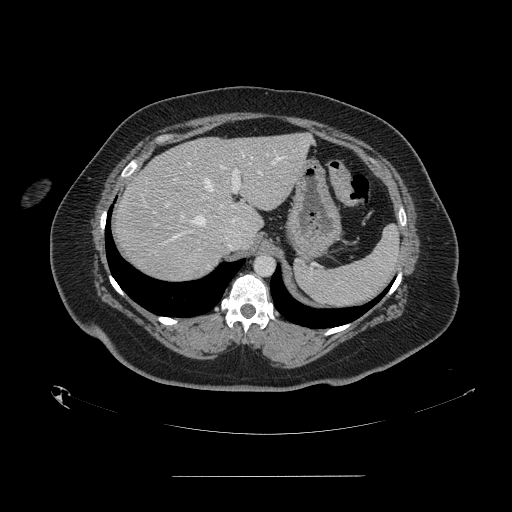
Contrast-enhanced abdominal CT, one axial slice; slice 113 of 164 in the series (ordered by position); 120 kVp; intravenous contrast given; soft-tissue window (W 400 / L 40 HU); 2.5 mm slice thickness; 512 × 512 image matrix. Female patient, age 52 years. Case-level facts recorded for this patient, not image findings: diagnosis: colorectal cancer liver metastases, imaged before liver resection; multiple liver metastases: yes; largest metastasis: 3.5 cm; disease in both lobes: no.
Outlined on this slice (outlined manually by an expert reader):
- hepatic veins: bounding box <153,155,285,238> (left, top, right, bottom; pixels)
- liver: <113,134,311,282>
- planned liver remnant (the part of the liver to remain after resection): <171,134,312,227>
- portal vein (with intrahepatic branches): <165,163,250,207>